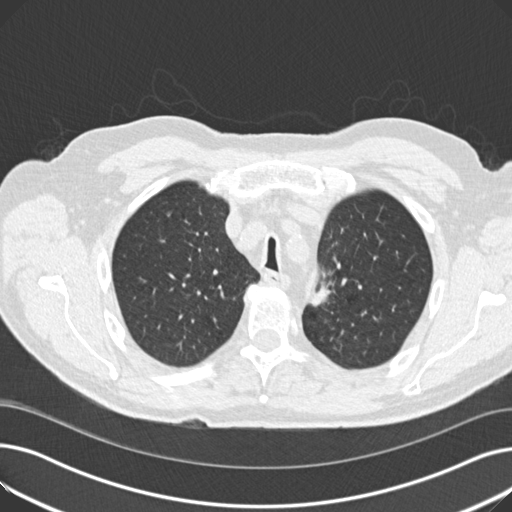
Low-dose screening chest CT, one axial slice; lung window (W 1500 / L -600 HU); 2 mm slice thickness; 512 × 512 image matrix, field of view 370 × 370 mm.
Outlined on this slice (manually delineated by an expert):
- lesion 1 (tumor, upper lobe of left lung): box from (x=311, y=285) to (x=330, y=306) px